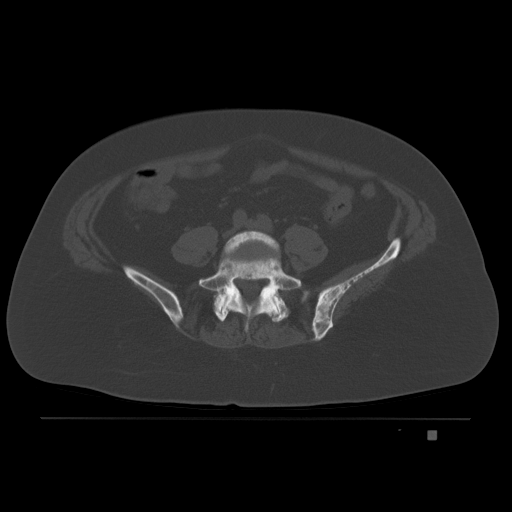
CT including the spine, one axial slice. Slice 32 of 221 in the series (ordered by position). Bone window (W 1800 / L 400 HU). 512 × 512 image matrix. Patient: female, 63 years. Case-level facts recorded for this patient, not image findings: primary cancer: breast.
Structures marked on this image (semi-automatically segmented with operator editing):
- L4 vertebra: bounding box (x1, y1, x2, y2) in pixels: (223, 230, 280, 324)
- L5 vertebra: (198, 257, 299, 333)